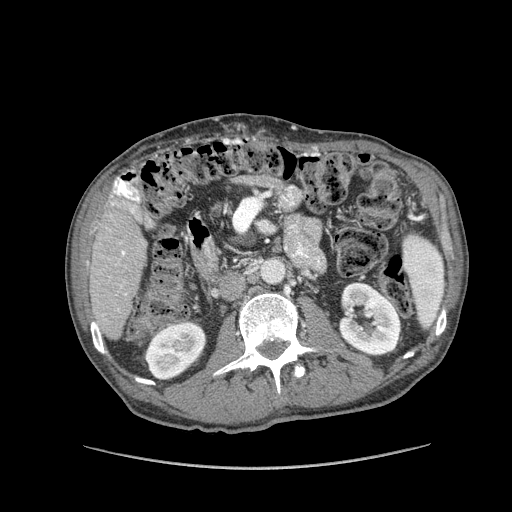
Contrast-enhanced abdominal CT (liver protocol), one axial slice. Slice 29 of 162 in the series (ordered by position). 100 kVp. Soft-tissue window (W 400 / L 40 HU). 2.5 mm slice thickness. 512 × 512 image matrix, field of view 400 × 400 mm. Case-level facts recorded for this patient, not image findings: diagnosis: hepatocellular carcinoma (patient treated with transarterial chemoembolisation; whether this scan precedes or follows treatment is not stated here); TNM stage (as recorded): Stage-IIIA; Child-Pugh class: A.
Outlined on this slice (semi-automatic segmentation, software-assisted and operator-edited):
- liver parenchyma outside the tumour (the mass and vessels are separate outlines, so this box may not span the whole liver): bounding box [x1, y1, x2, y2] px = [90, 193, 146, 338]
- liver vessels: [111, 203, 126, 255]